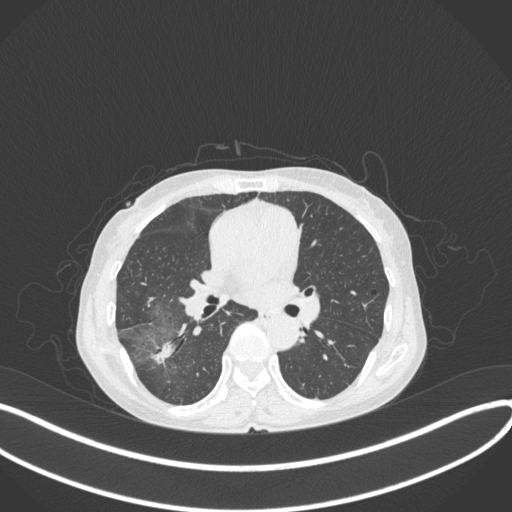
Chest CT, one axial slice; position 212 of 379 along the scan axis; reconstruction kernel B31f; 120 kVp; lung window (W 1500 / L -600 HU); 1 mm slice thickness; 512 × 512 image matrix, field of view 400 × 400 mm. Female patient, age 69 years. From the clinical record (not read from this slice): clinical TNM (as recorded): T1b N0 M0; histopathological grade: G2-3.
Outlined on this slice (rectangle marked by the reading radiologist):
- lung tumour (recorded histology: adenocarcinoma): box from (x=141, y=334) to (x=183, y=370) px